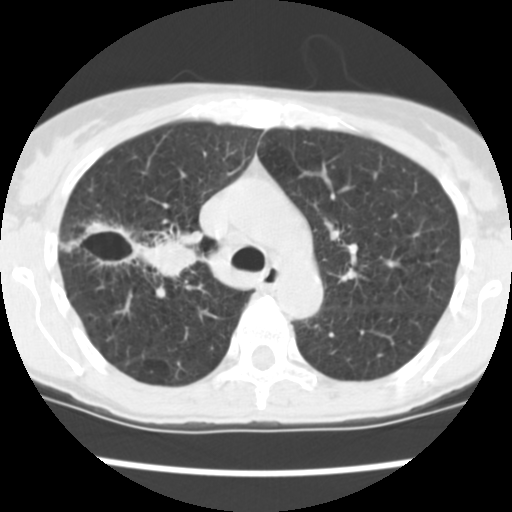
Low-dose screening chest CT, axial slice, baseline annual screen, lung window (W 1500 / L -600 HU), 2.5 mm slice thickness, standard (soft-tissue) reconstruction kernel (STANDARD). Female participant, aged 60 years at enrolment.
Expert reader's lesion annotation, bounding box <83,216,195,284> (left, top, right, bottom; pixels). The screening reader recorded 3 non-calcified nodules or masses ≥4 mm on this exam; which of them this box marks is not recorded. Official screen result: positive, change unspecified: nodule(s) >= 4 mm or enlarging nodule(s), mass(es), or other non-specific abnormalities suspicious for lung cancer. Participant outcome: lung cancer diagnosed 19 days after this screen — non-small cell carcinoma, right upper lobe, stage IV (AJCC 6th edition), 26 mm at pathology.